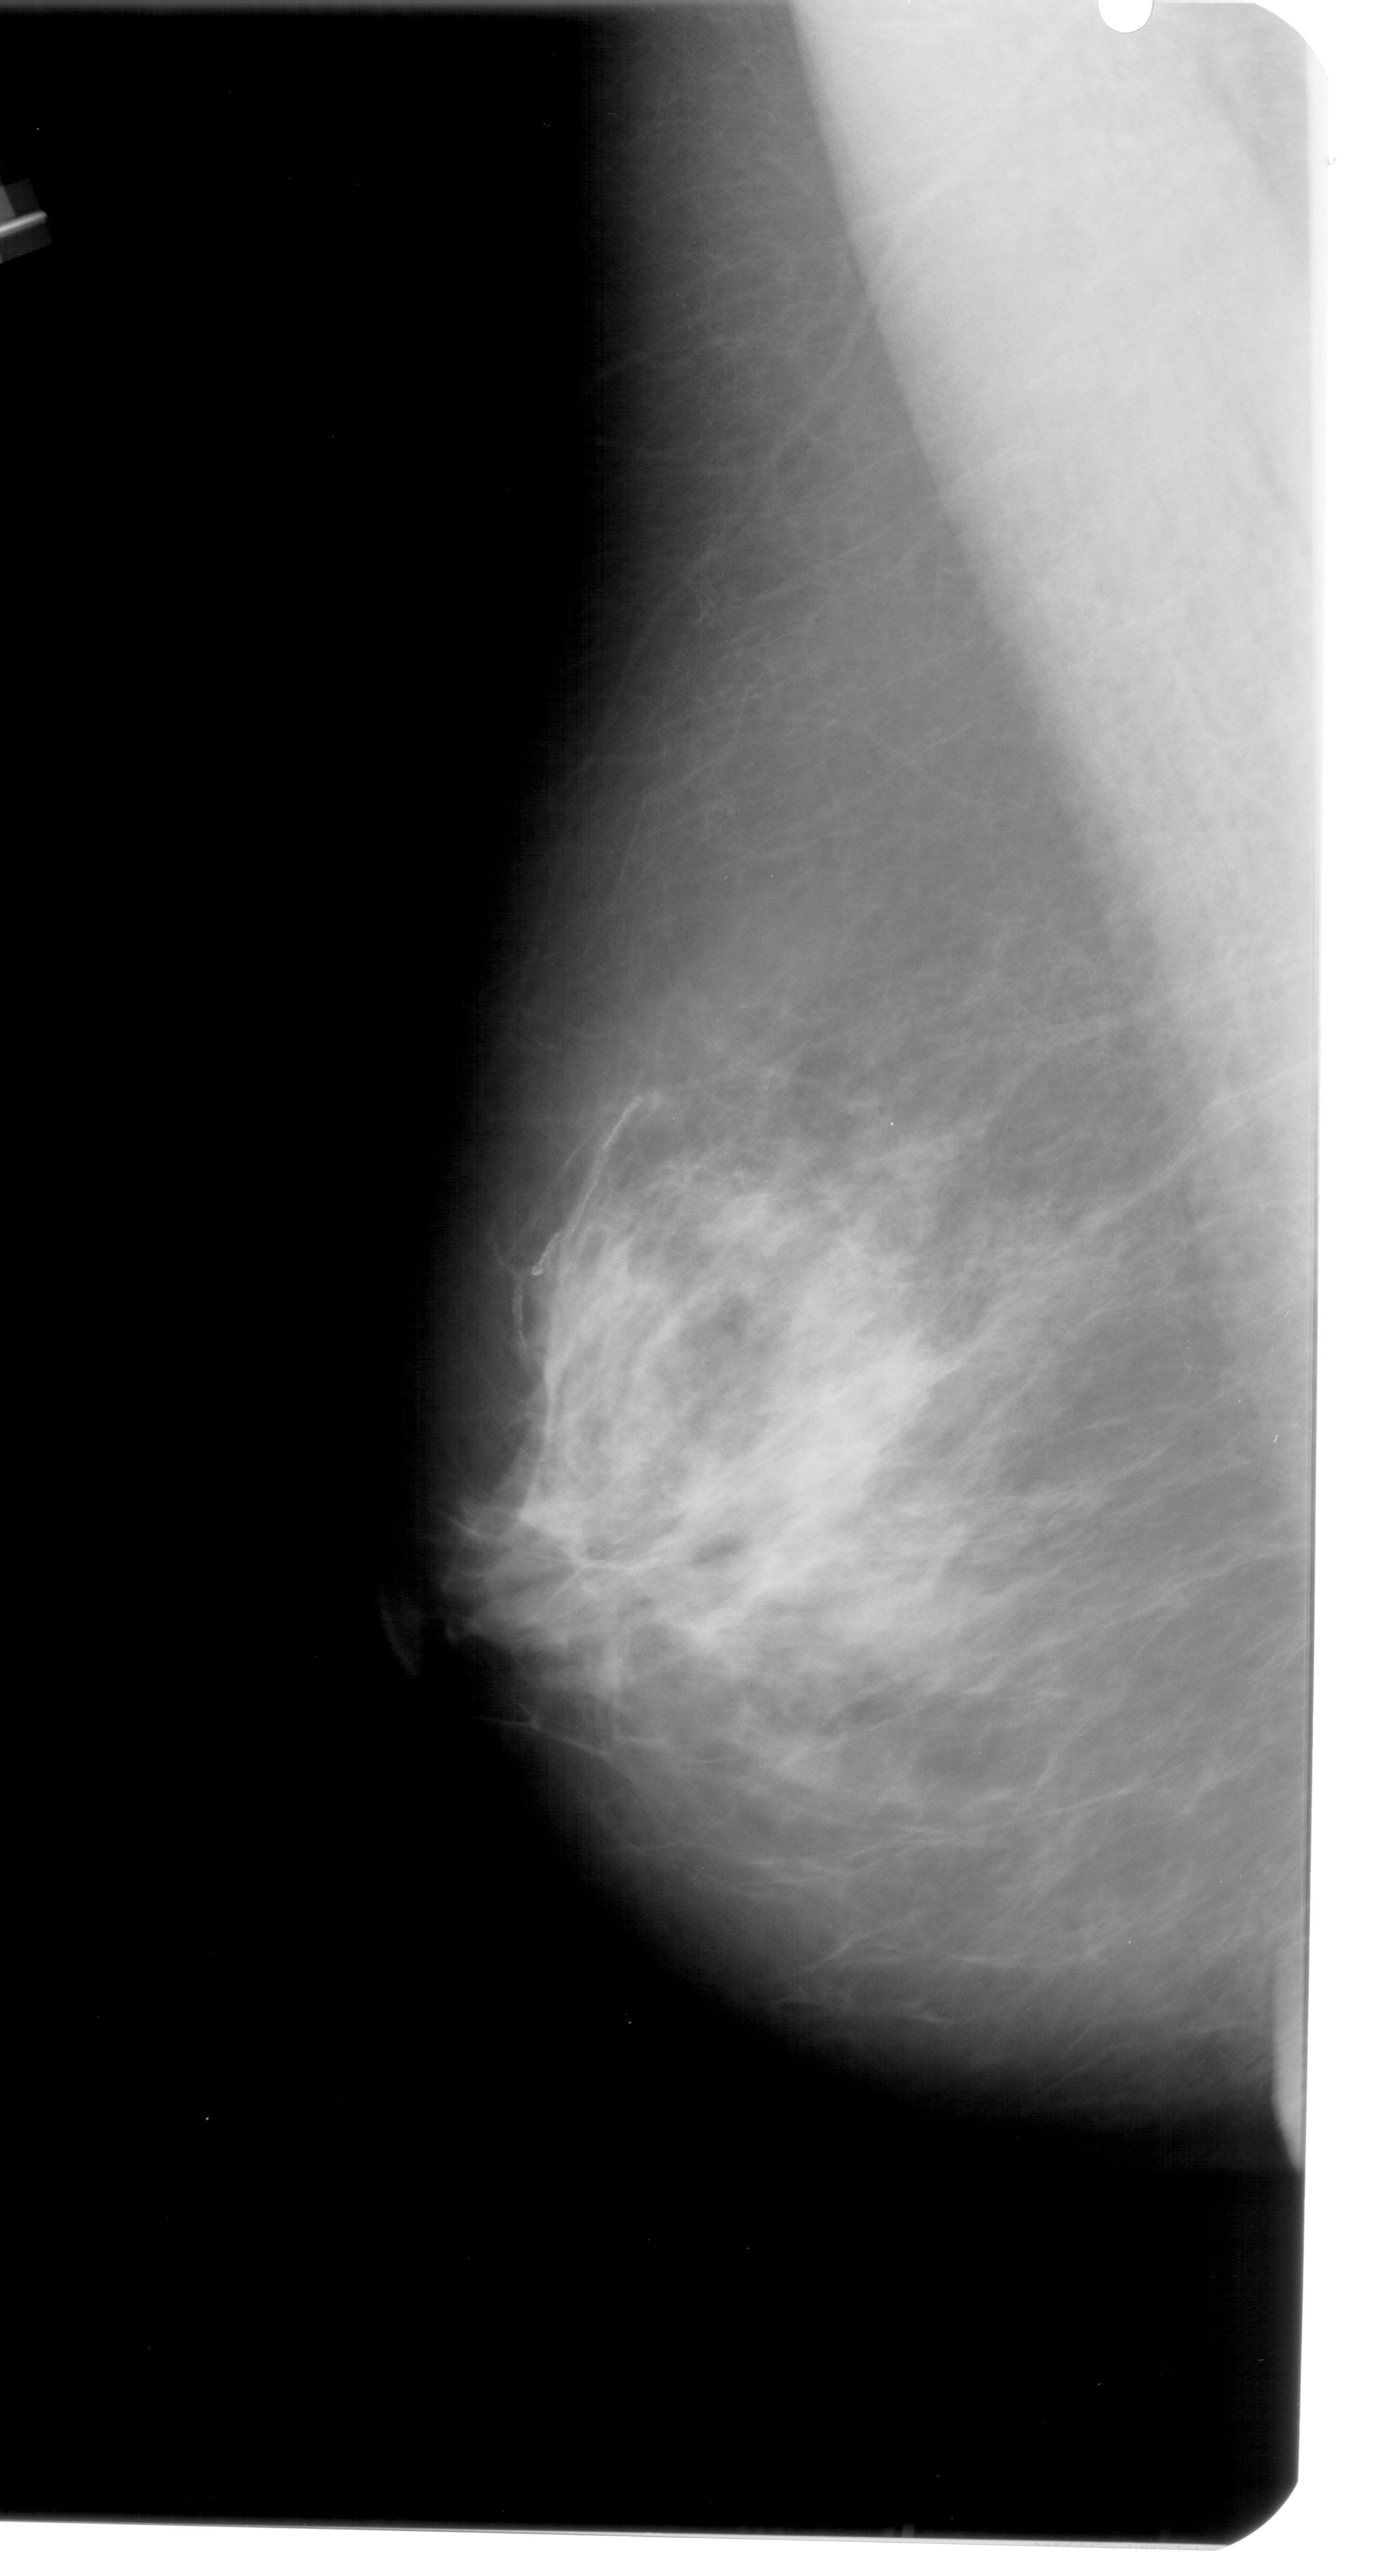
Mammogram (digitized film); left breast; MLO view; breast composition: heterogeneously dense (BI-RADS density category 3 of 4); 1373 × 2576 image matrix.
Expert-marked regions of interest on this film, with their recorded descriptors:
- calcifications, morphology pleomorphic, distribution clustered; BI-RADS assessment category 4; subtlety rating 1 on a 1 (subtle) to 5 (obvious) scale; pathology result (as recorded, not read from the image): benign: bounding box [x1, y1, x2, y2] px = [700, 1154, 829, 1249]